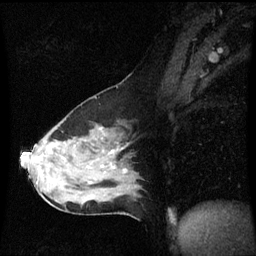
Breast MRI (dynamic contrast-enhanced), one sagittal slice. Dynamic contrast-enhanced series, image 2 of 3 at this slice position (ordered by acquisition). 1.5 T. TE 4.2 ms, TR 8.9 ms. 2 mm slice thickness. 256 × 256 image matrix, field of view 210 × 210 mm. Female patient, age 50 years. Case-level facts recorded for this patient, not image findings: setting: breast cancer imaged before/during neoadjuvant chemotherapy; receptor status: HR-positive, HER2-negative.
Structures marked on this image (semi-automatic segmentation, software-assisted and operator-edited):
- analysis volume of interest (the breast-tissue region the enhancement analysis was run in; not a lesion): bounding box (x1, y1, x2, y2) in pixels: (21, 99, 142, 210)
- tumour enhancement mask (voxels above the 70 % enhancement threshold inside the analysis volume of interest): (111, 152, 114, 154)